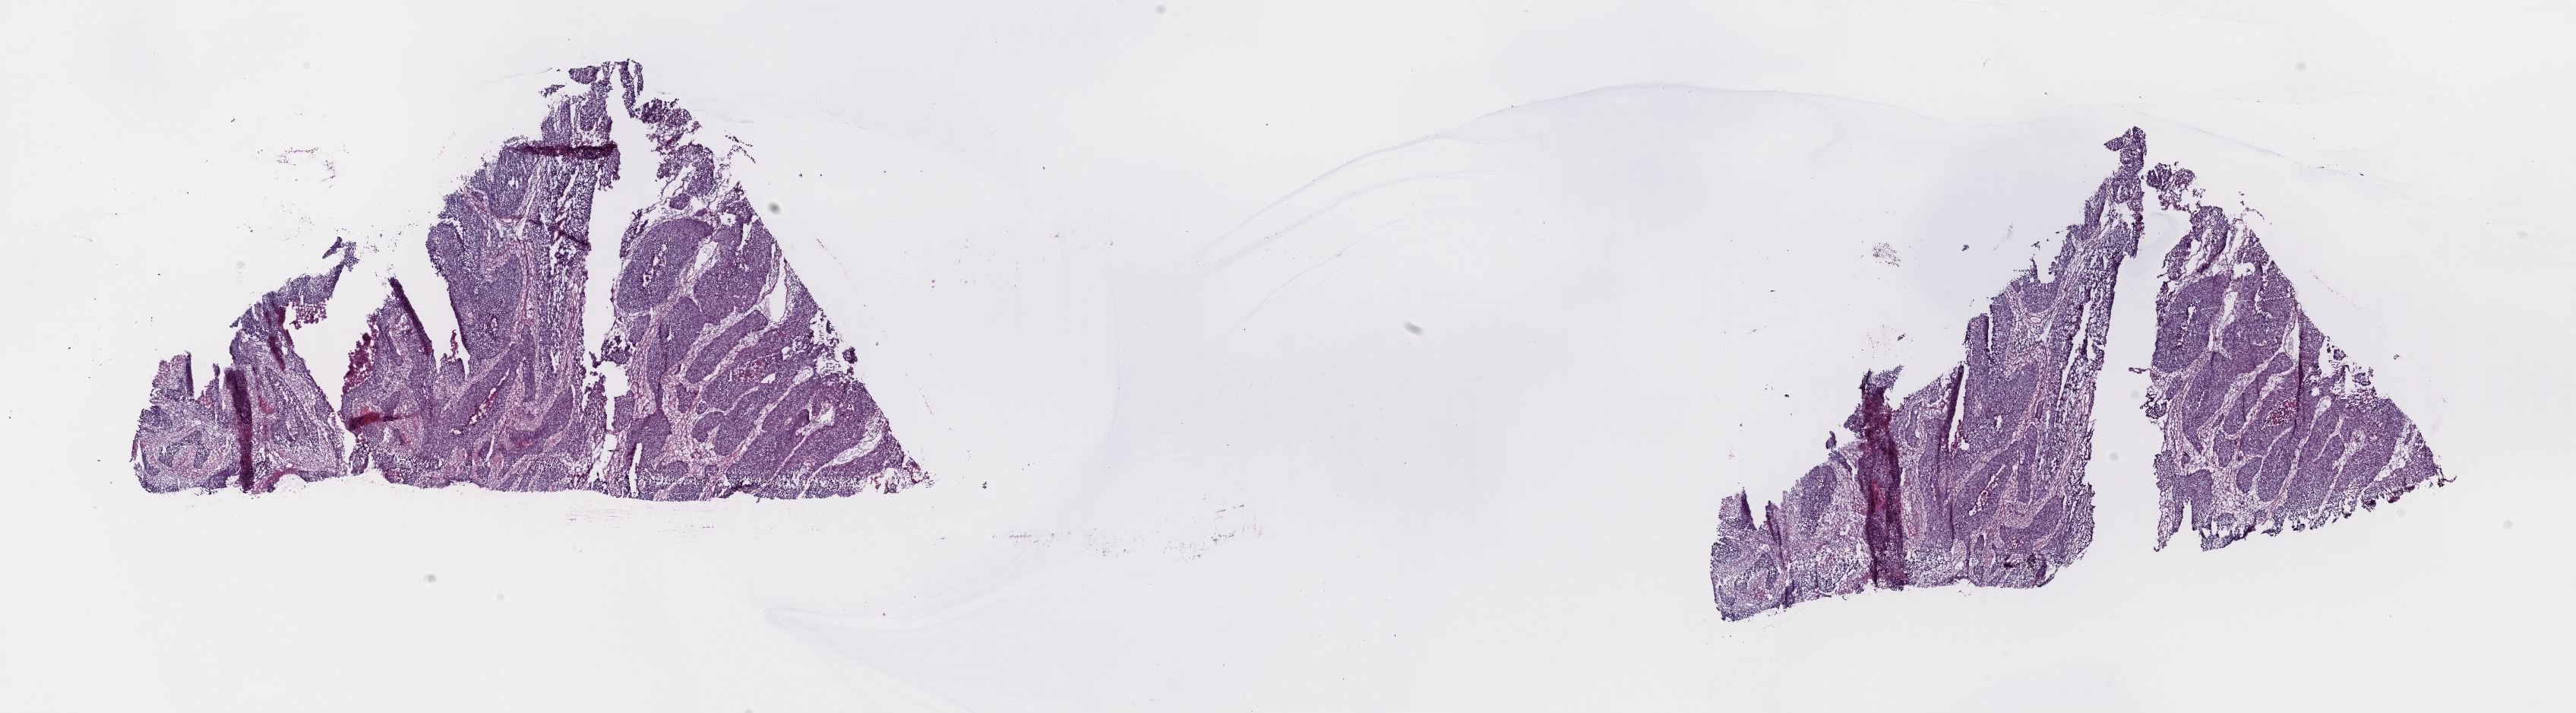
H&E whole-slide image, low-resolution overview of the scanned area, about 26.8 x 7.4 mm. Frozen section. Primary tumour sample from the bladder. Female patient; age at initial diagnosis 59 years. Histologic grade: high grade. Pathologist review of this section (percent, as recorded): tumour cells 60%, tumour nuclei 60%, normal cells 0%, stromal cells 35%, necrosis 5%. Infiltration values recorded for this section: lymphocyte infiltration 0%, monocyte infiltration 0%, neutrophil infiltration 0%.
AJCC pathologic stage: IV (6th edition). Pathologic diagnosis: Transitional cell carcinoma (lateral wall of bladder). TNM: T4a N2 M0.